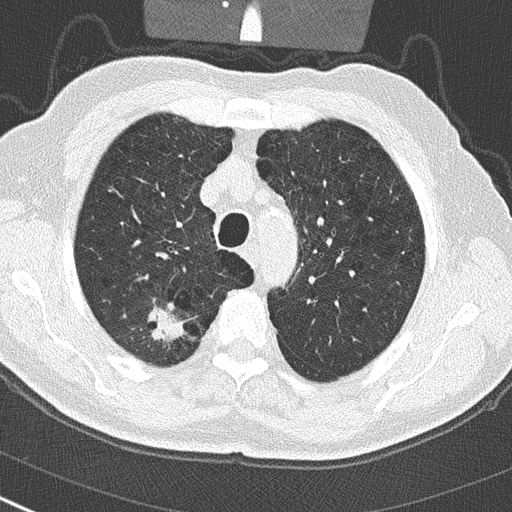
Chest CT (low-dose screening protocol), one axial image, baseline screening round, lung window (W 1500 / L -600 HU), 120 kVp, slice 67 of 290 in the series, 512 × 512 image matrix, field of view 300 × 300 mm. Male participant, aged 65 years at enrolment. Current smoker at enrolment.
Expert reader's lesion annotation, bounding box (x1, y1, x2, y2) in pixels: (131, 300, 196, 358). Reader record for this screening exam (exam-level; its link to the box is not recorded): non-calcified nodule or mass ≥4 mm, right upper lobe, 24 × 19 mm, spiculated (stellate) margins, soft tissue attenuation. Official screen result: positive, change unspecified: nodule(s) >= 4 mm or enlarging nodule(s), mass(es), or other non-specific abnormalities suspicious for lung cancer. Later outcome: lung cancer diagnosed 32 days after this screen — non-small cell carcinoma, right upper lobe, poorly differentiated (G3), stage IA (AJCC 6th edition), 29 mm at pathology.